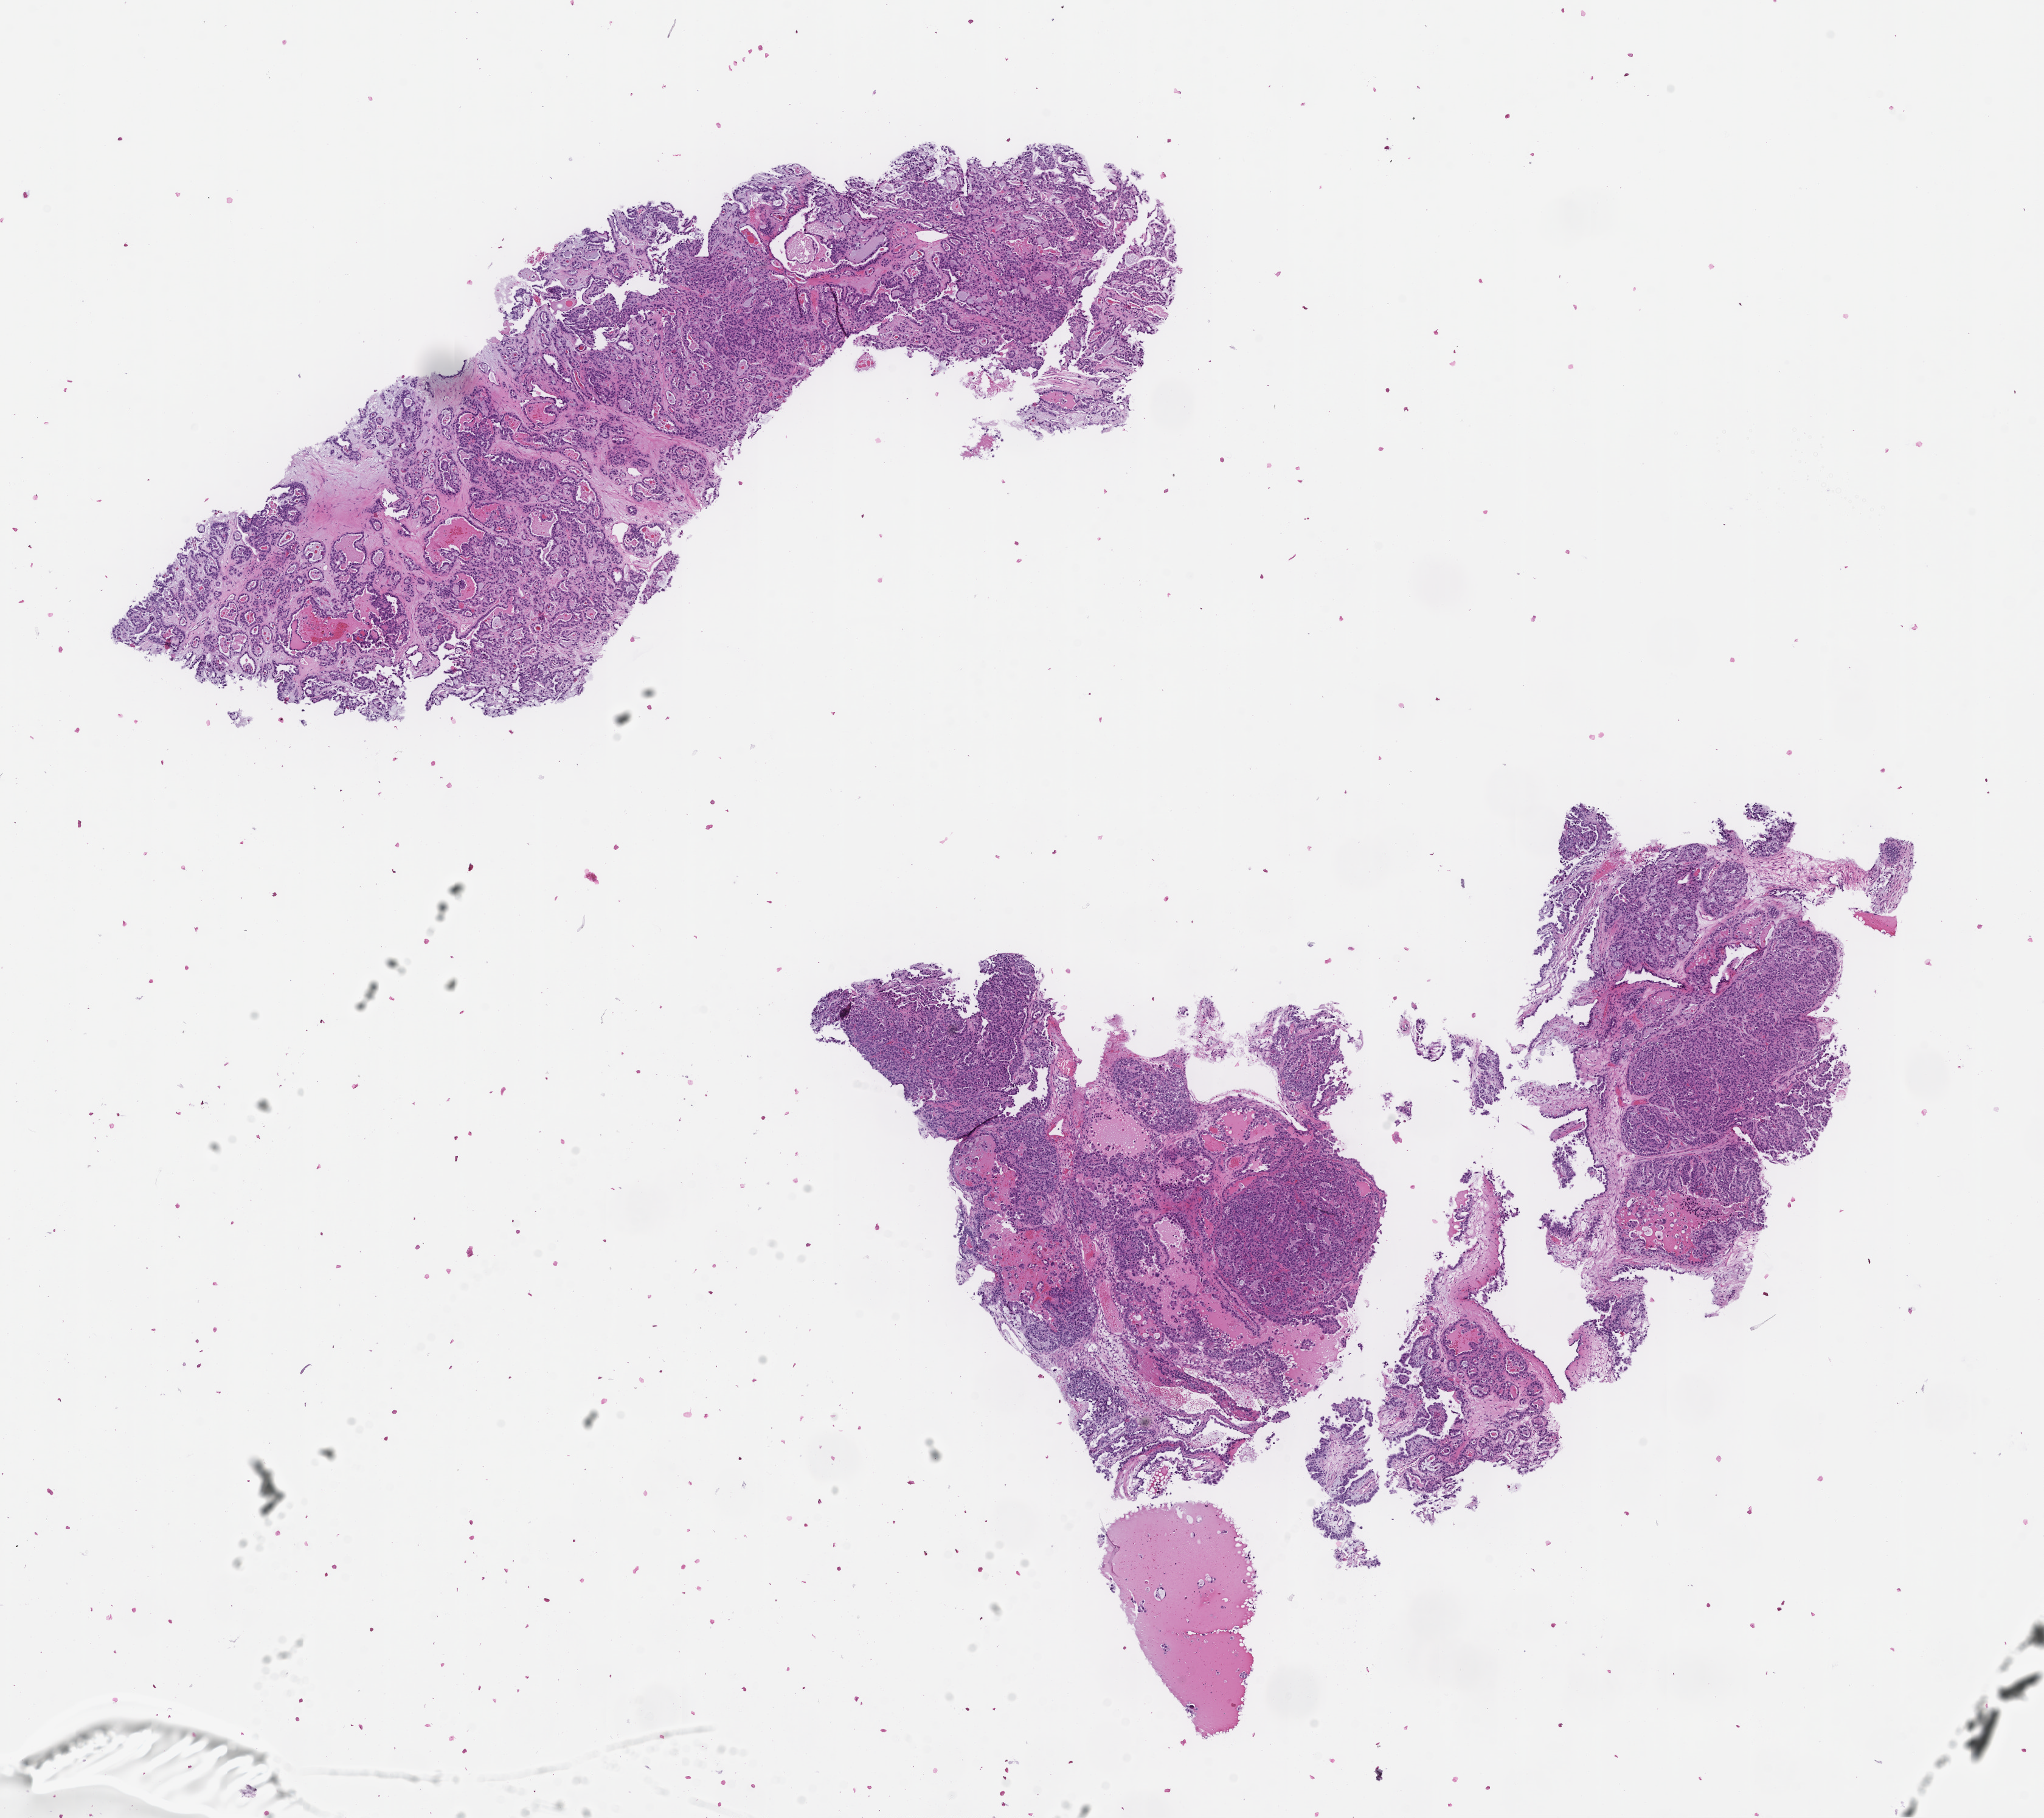
Hematoxylin and eosin (H&E) whole-slide image, shown as a low-resolution overview of the whole scanned area (about 13.6 x 12.1 mm), formalin-fixed, paraffin-embedded (FFPE) tissue, tissue site: ovary. Female patient.
- this section: primary tumor
- diagnosis: Ovarian Carcinoma